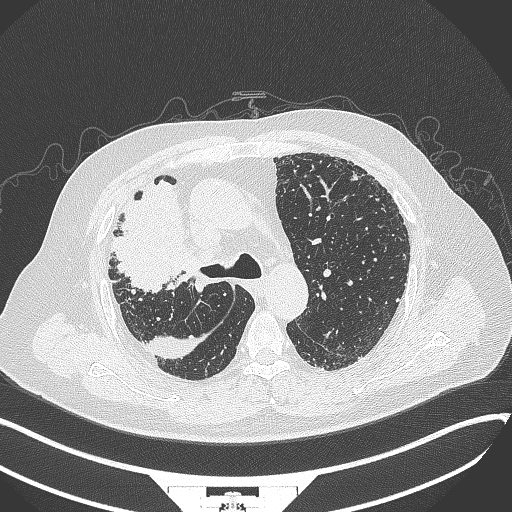
Chest CT, one axial slice; slice 241 of 384 in the series (ordered by position); reconstruction kernel B70f; 120 kVp; lung window (W 1500 / L -600 HU); 1 mm slice thickness; 512 × 512 image matrix, field of view 400 × 400 mm. Patient: male, 69 years. Case-level facts recorded for this patient, not image findings: clinical TNM (as recorded): T4 N3 M1.
Structures marked on this image (rectangle marked by the reading radiologist):
- lung tumour (recorded histology: adenocarcinoma): box from (x=106, y=180) to (x=194, y=300) px